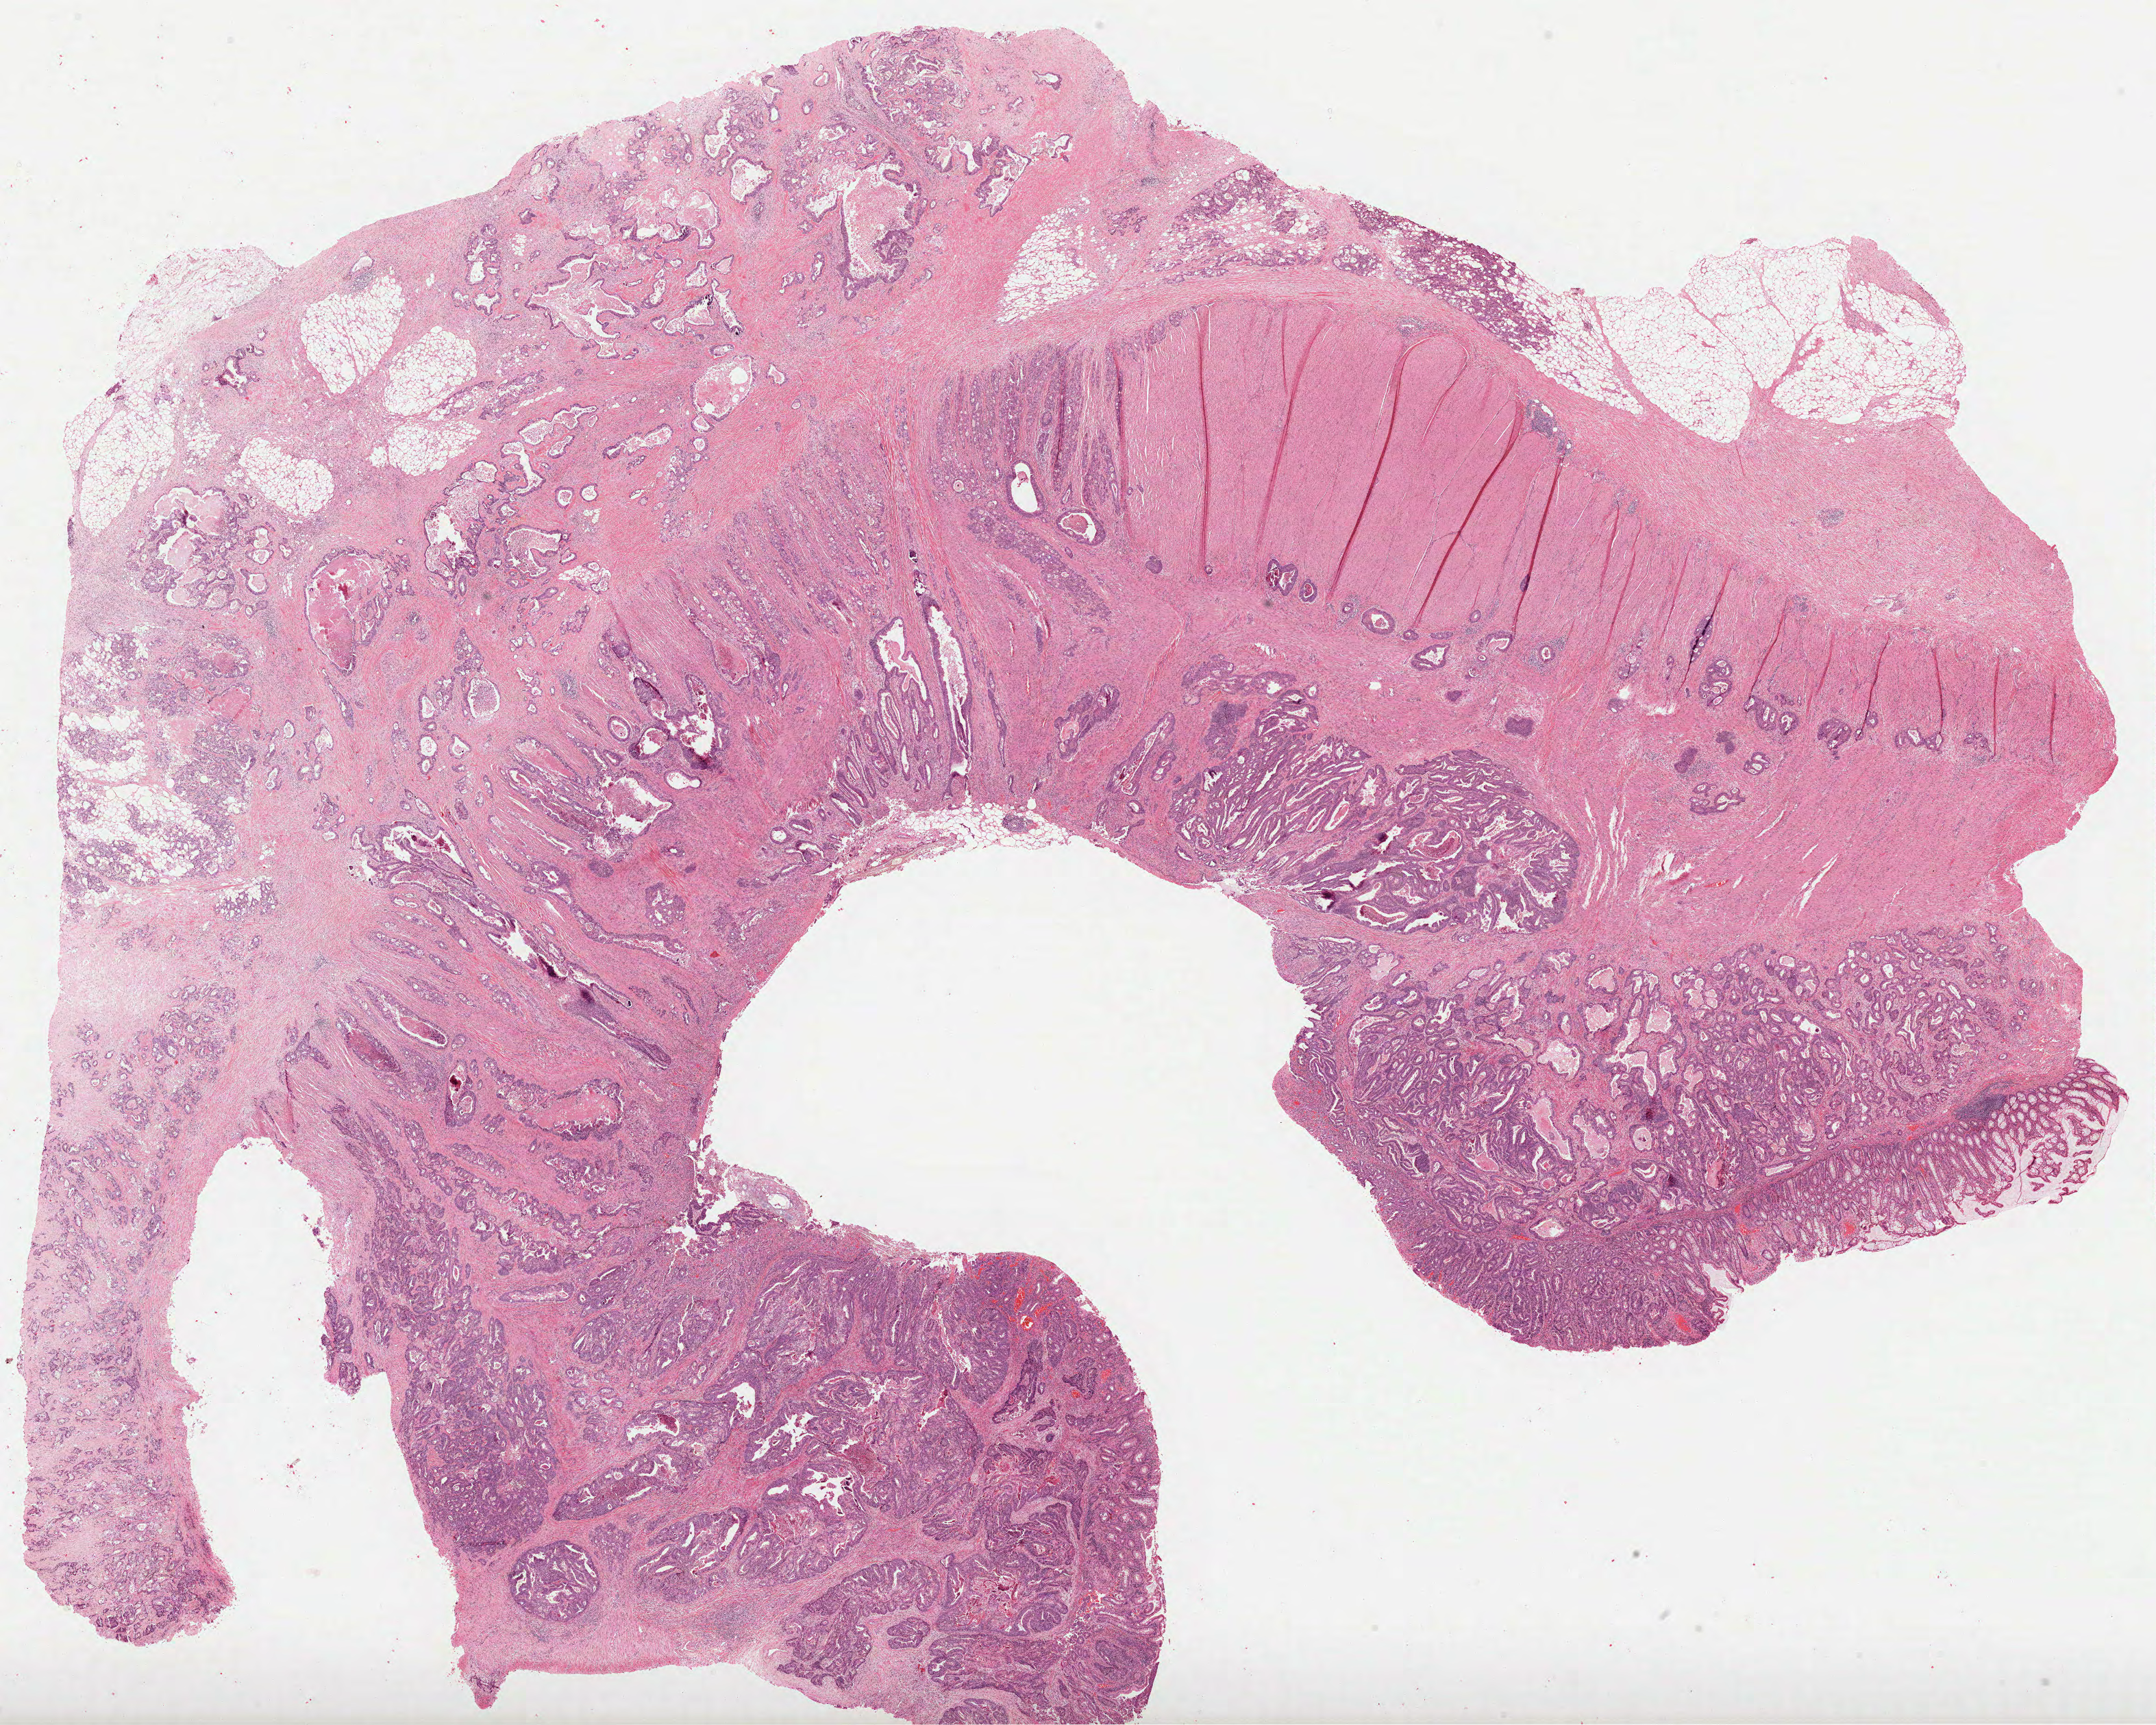
H&E whole-slide image, shown as a low-resolution overview of the whole scanned area (about 25.4 x 20.3 mm), formalin-fixed paraffin-embedded (FFPE) diagnostic section, sample: primary tumour, colon. Female, age 61 years at initial diagnosis.
* histologic diagnosis: Adenocarcinoma, NOS (sigmoid colon)
* lymph nodes positive (case pathology): 6 of 6 examined
* AJCC pathologic stage: IIIB (7th edition)